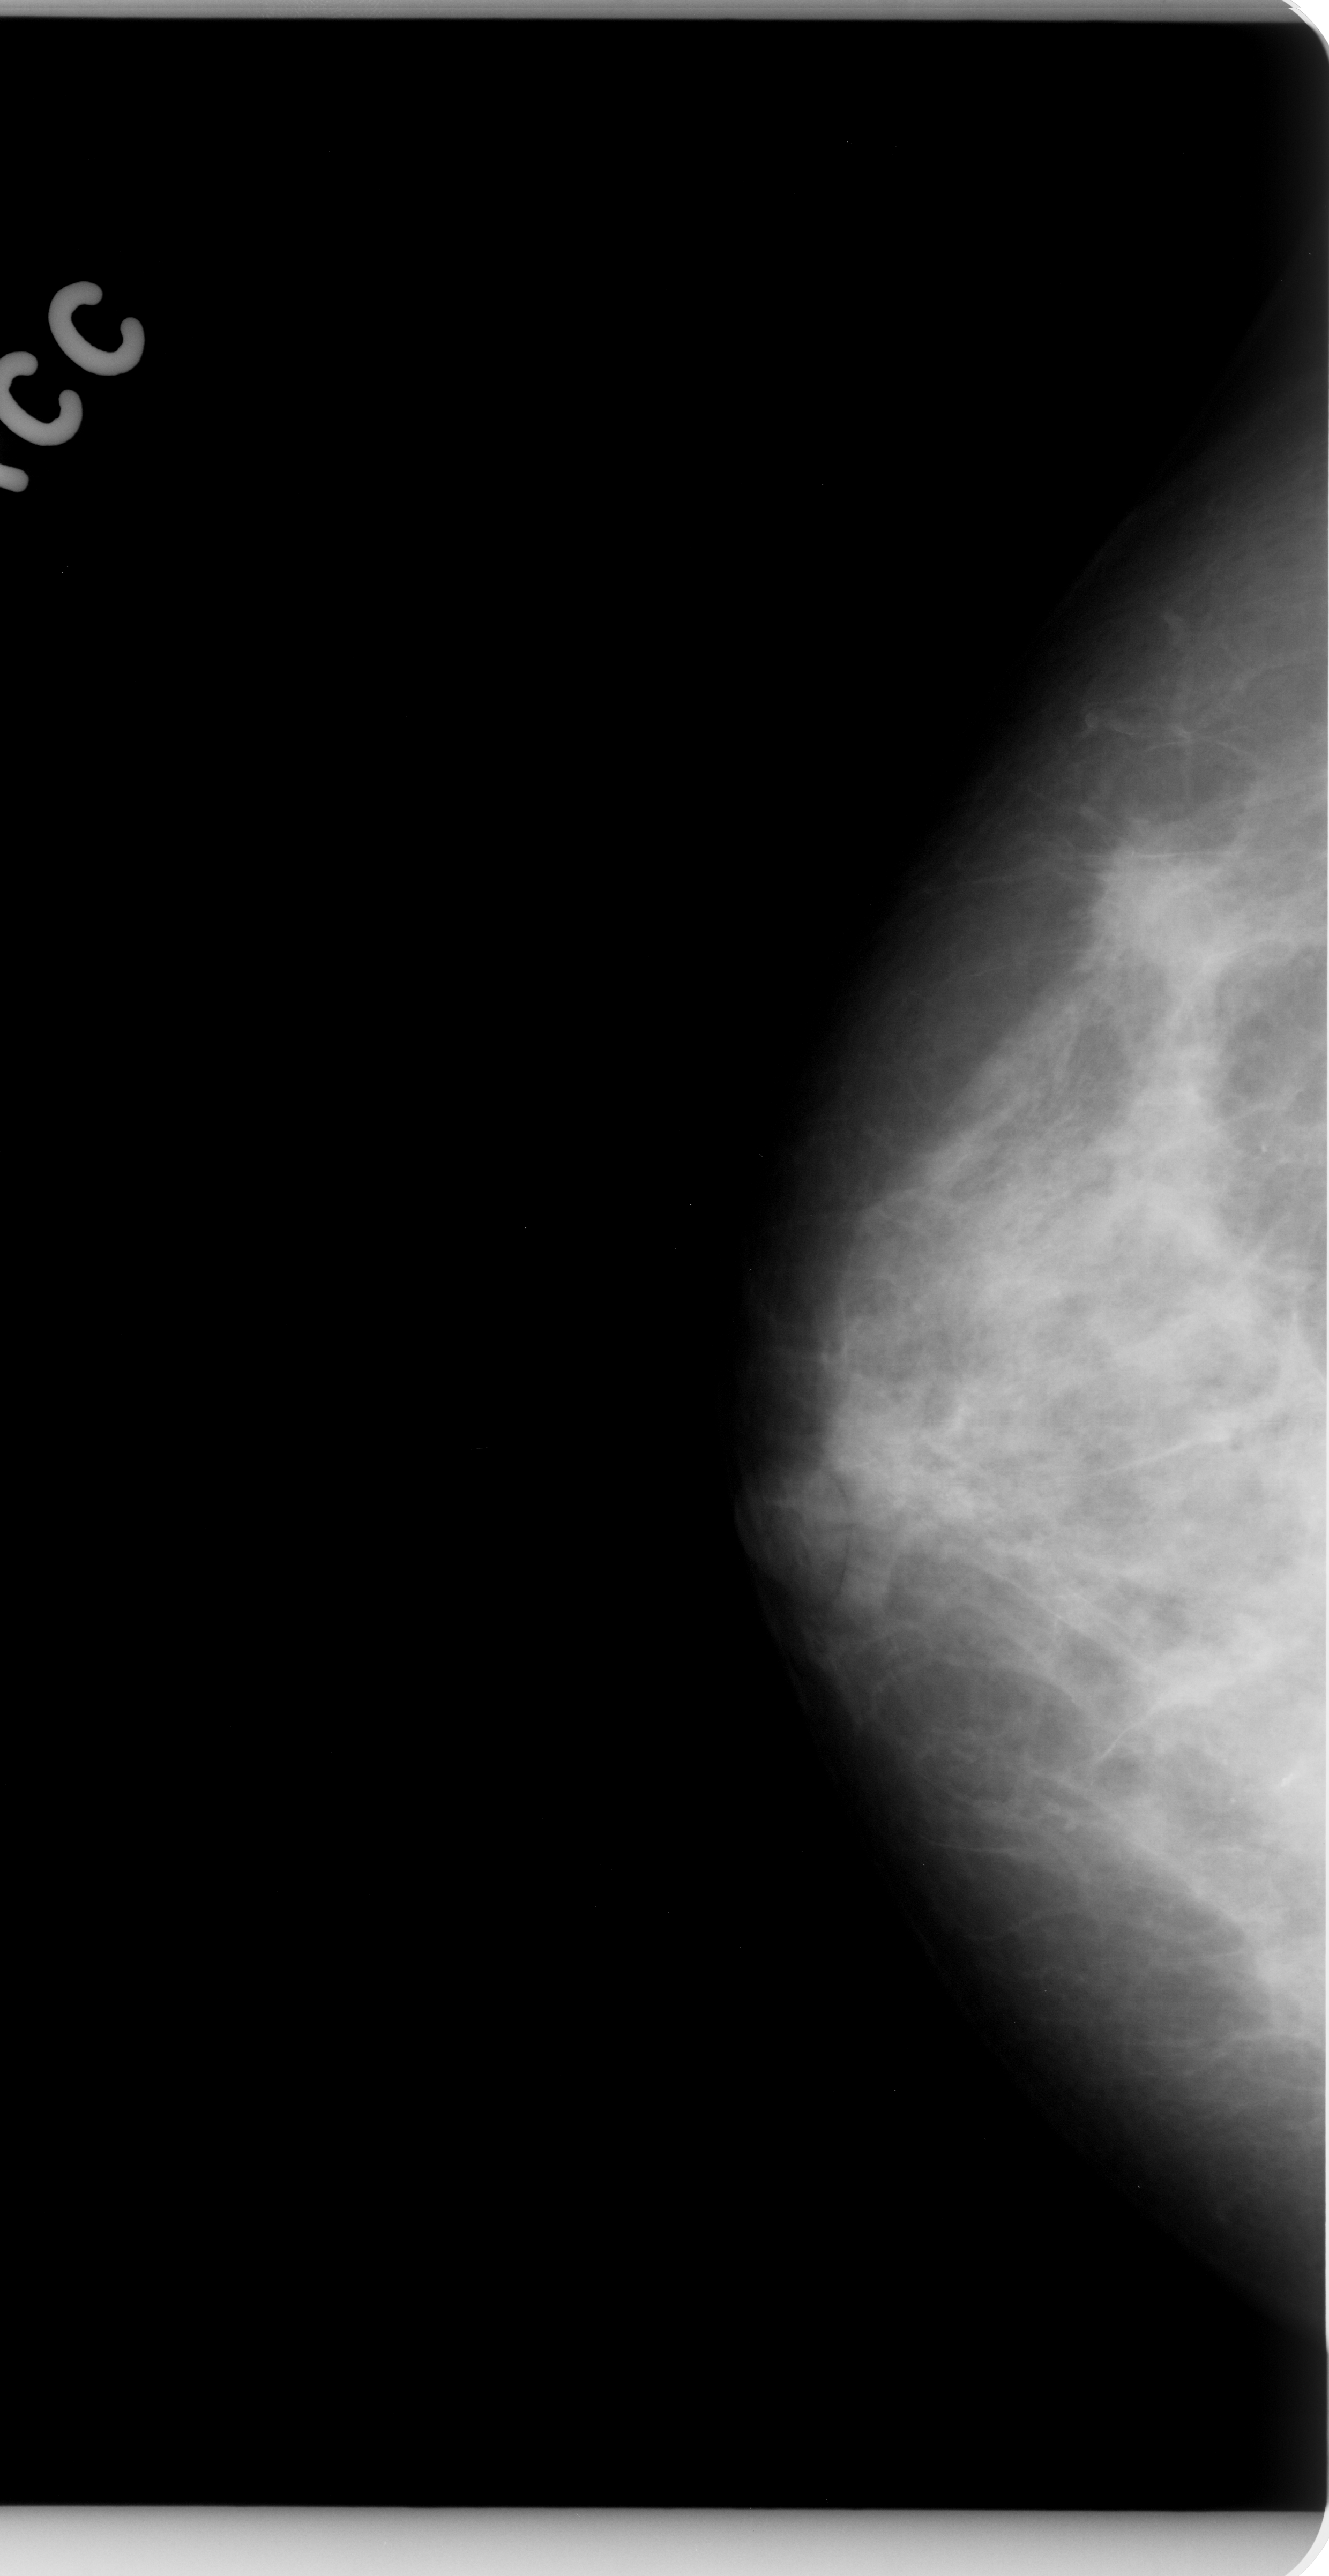
Scanned film-screen mammogram; right breast; CC view; breast composition: heterogeneously dense (BI-RADS density category 3 of 4); 1329 × 2576 image matrix.
Expert-marked regions of interest on this film, with their recorded descriptors:
- mass, shape irregular, margins ill defined; BI-RADS assessment category 4; pathology result (as recorded, not read from the image): malignant: bounding box [x1, y1, x2, y2] px = [1100, 827, 1255, 999]